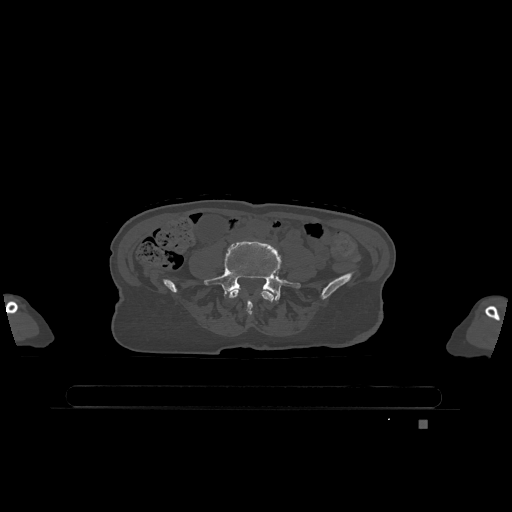
CT including the spine, one axial slice; slice 258 of 1317 in the series (ordered by position); bone window (W 1800 / L 400 HU); 512 × 512 image matrix. Patient: female, 74 years. From the clinical record (not read from this slice): primary cancer: lung; vertebrae with lytic lesions (as recorded): T1, T4, T5, T6, L4, L5.
Structures marked on this image (semi-automatic segmentation, software-assisted and operator-edited):
- L4 vertebra: bounding box <229,289,274,316> (left, top, right, bottom; pixels)
- L5 vertebra: <204,241,301,303>